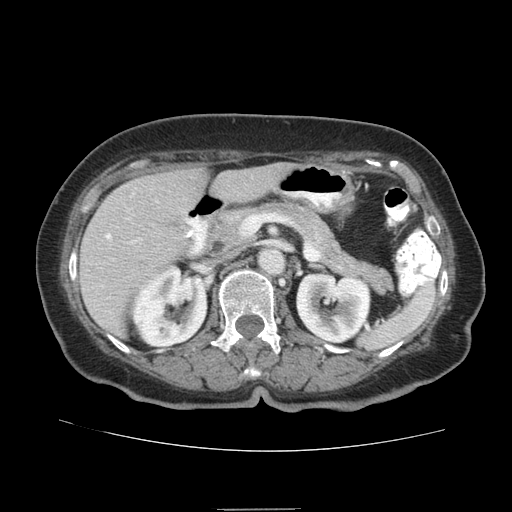
Contrast-enhanced abdominal CT (liver protocol), one axial slice. Soft-tissue window (W 400 / L 40 HU). 512 × 512 image matrix, field of view 360 × 360 mm. Case-level facts recorded for this patient, not image findings: diagnosis: hepatocellular carcinoma (patient treated with transarterial chemoembolisation; whether this scan precedes or follows treatment is not stated here); TNM stage (as recorded): Stage-IVA; Child-Pugh class: B; tumour nodularity: uninodular.
Structures marked on this image (semi-automatic segmentation, software-assisted and operator-edited):
- liver parenchyma outside the tumour (the mass and vessels are separate outlines, so this box may not span the whole liver): bounding box <80,162,291,334> (left, top, right, bottom; pixels)
- liver vessels: <106,218,207,253>